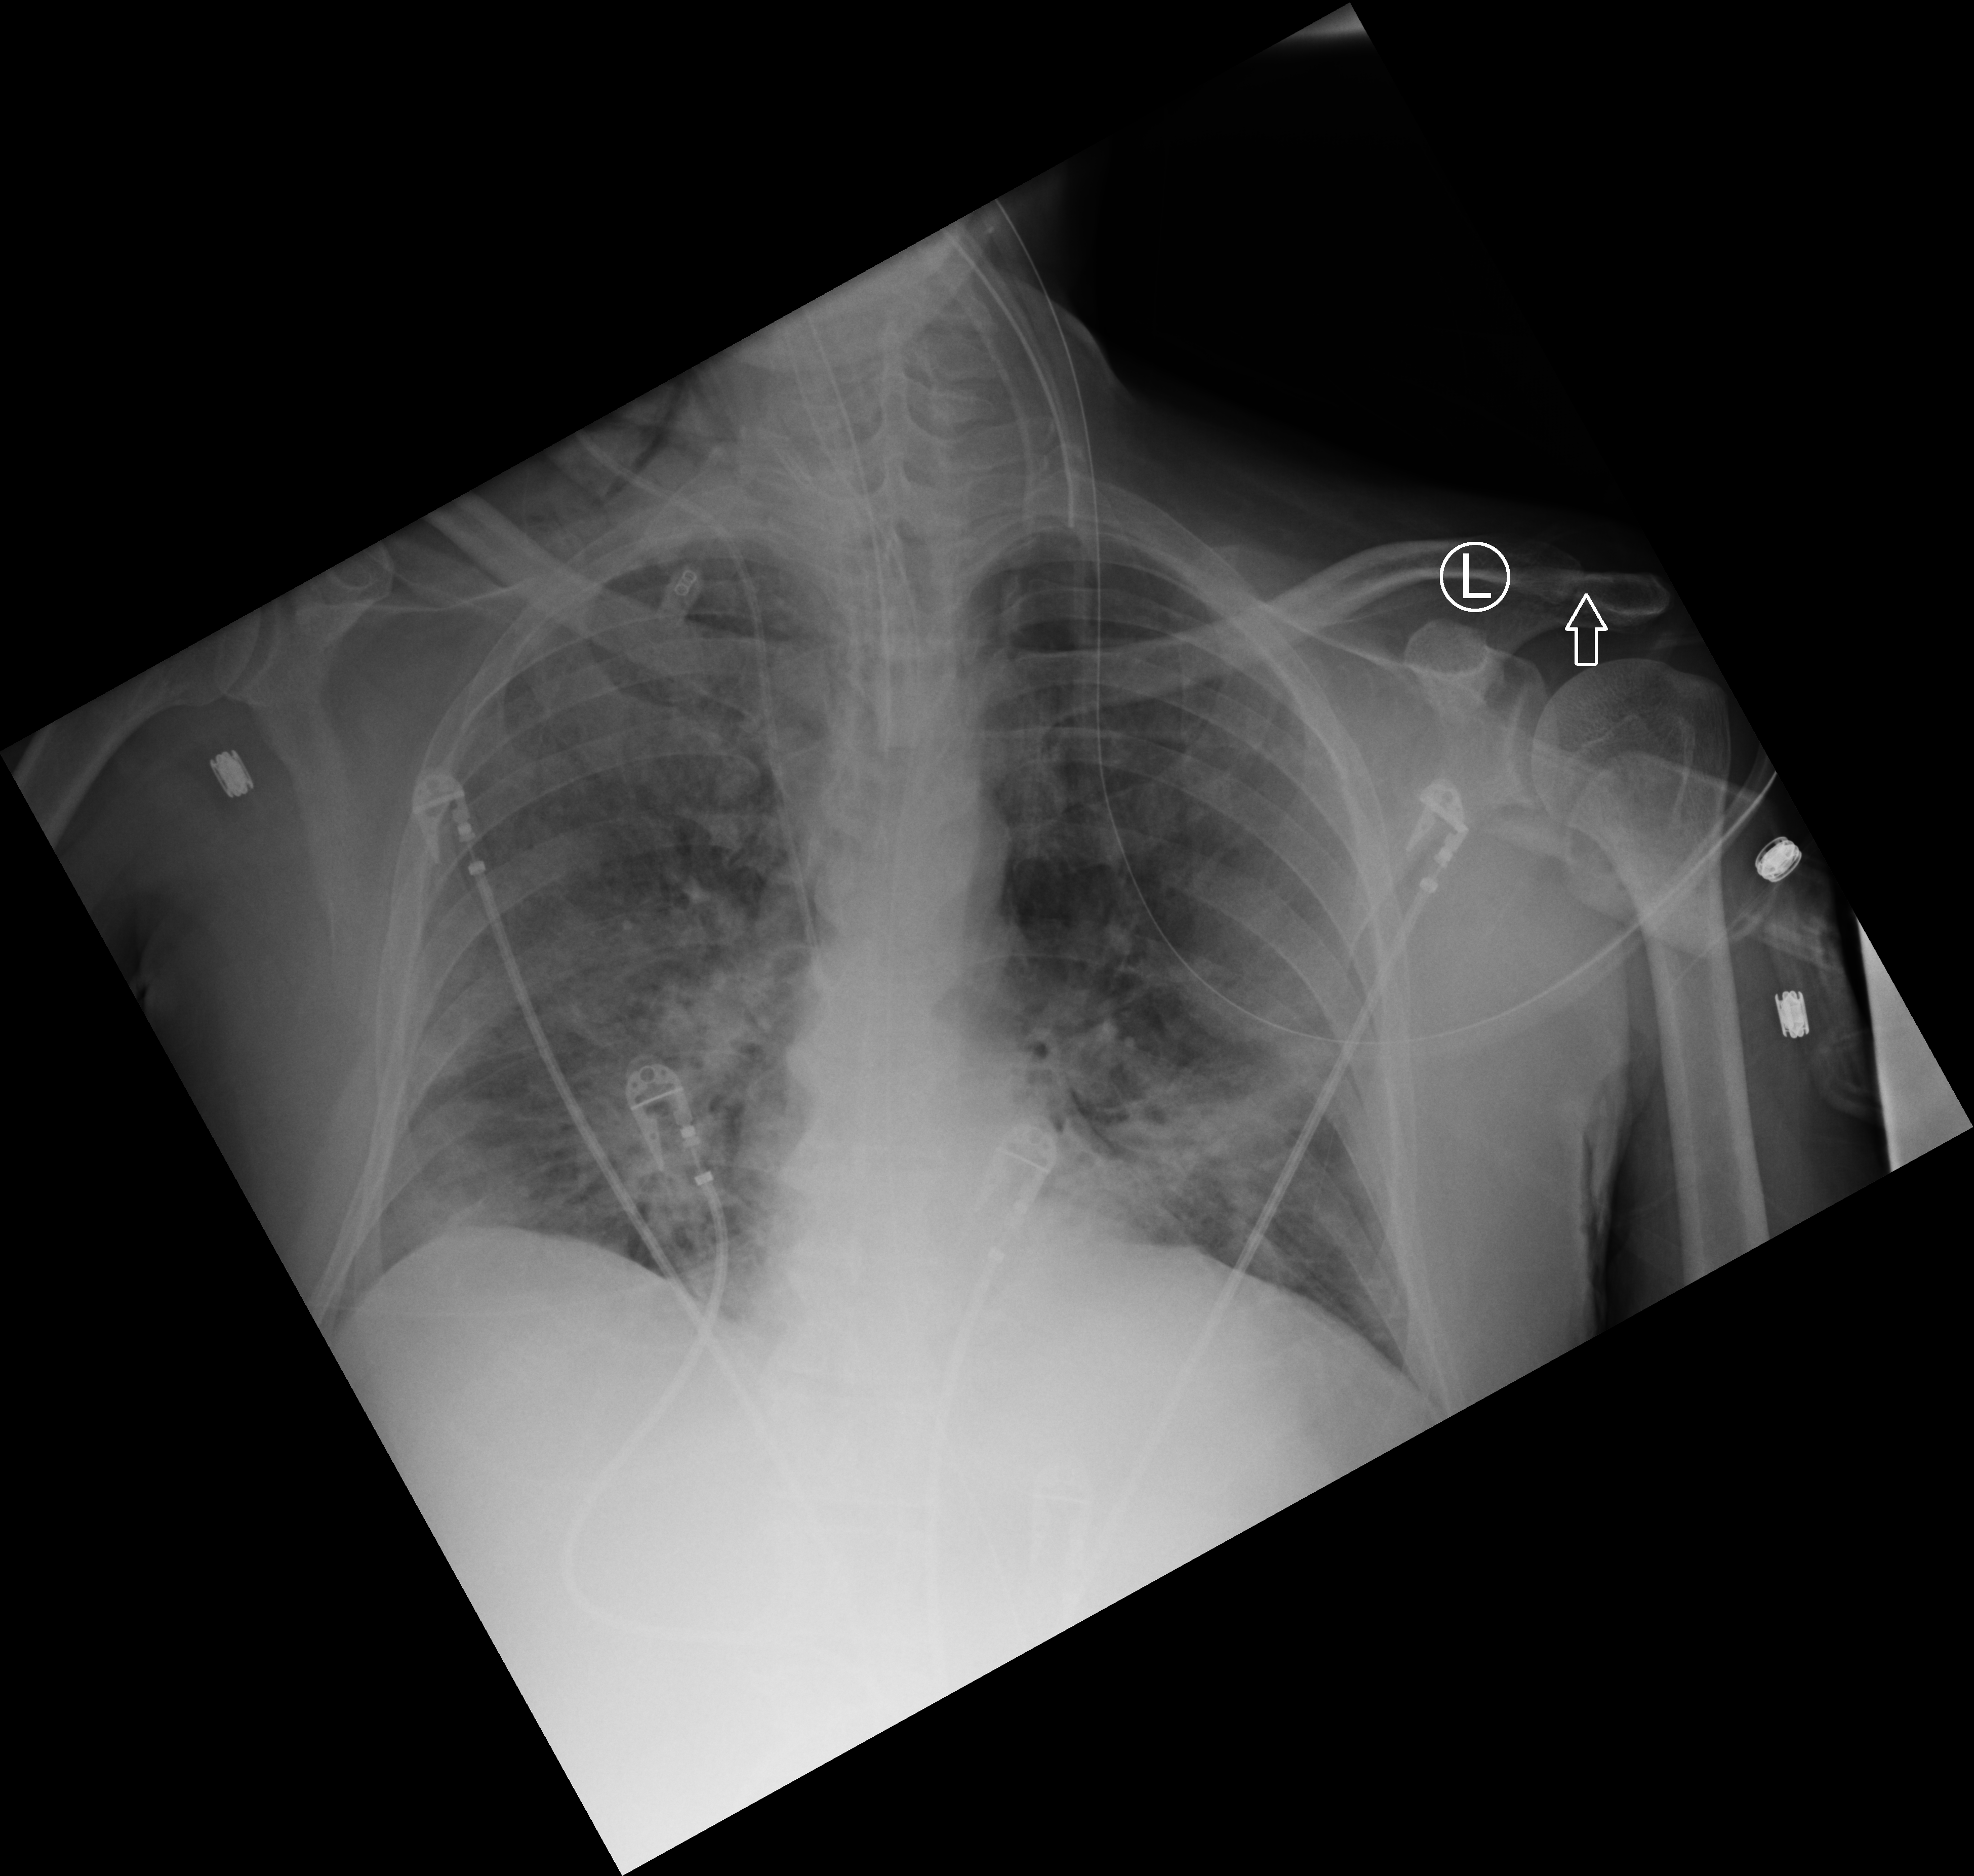
Chest X-ray (portable), anteroposterior (AP) projection. Patient hospitalised with COVID-19; male, aged 60–74 years.
From the hospital-stay record, not from the radiograph (when in the stay this image was taken is not recorded):
- admitted to intensive care during this hospital stay: yes
- length of hospital stay: 15 days